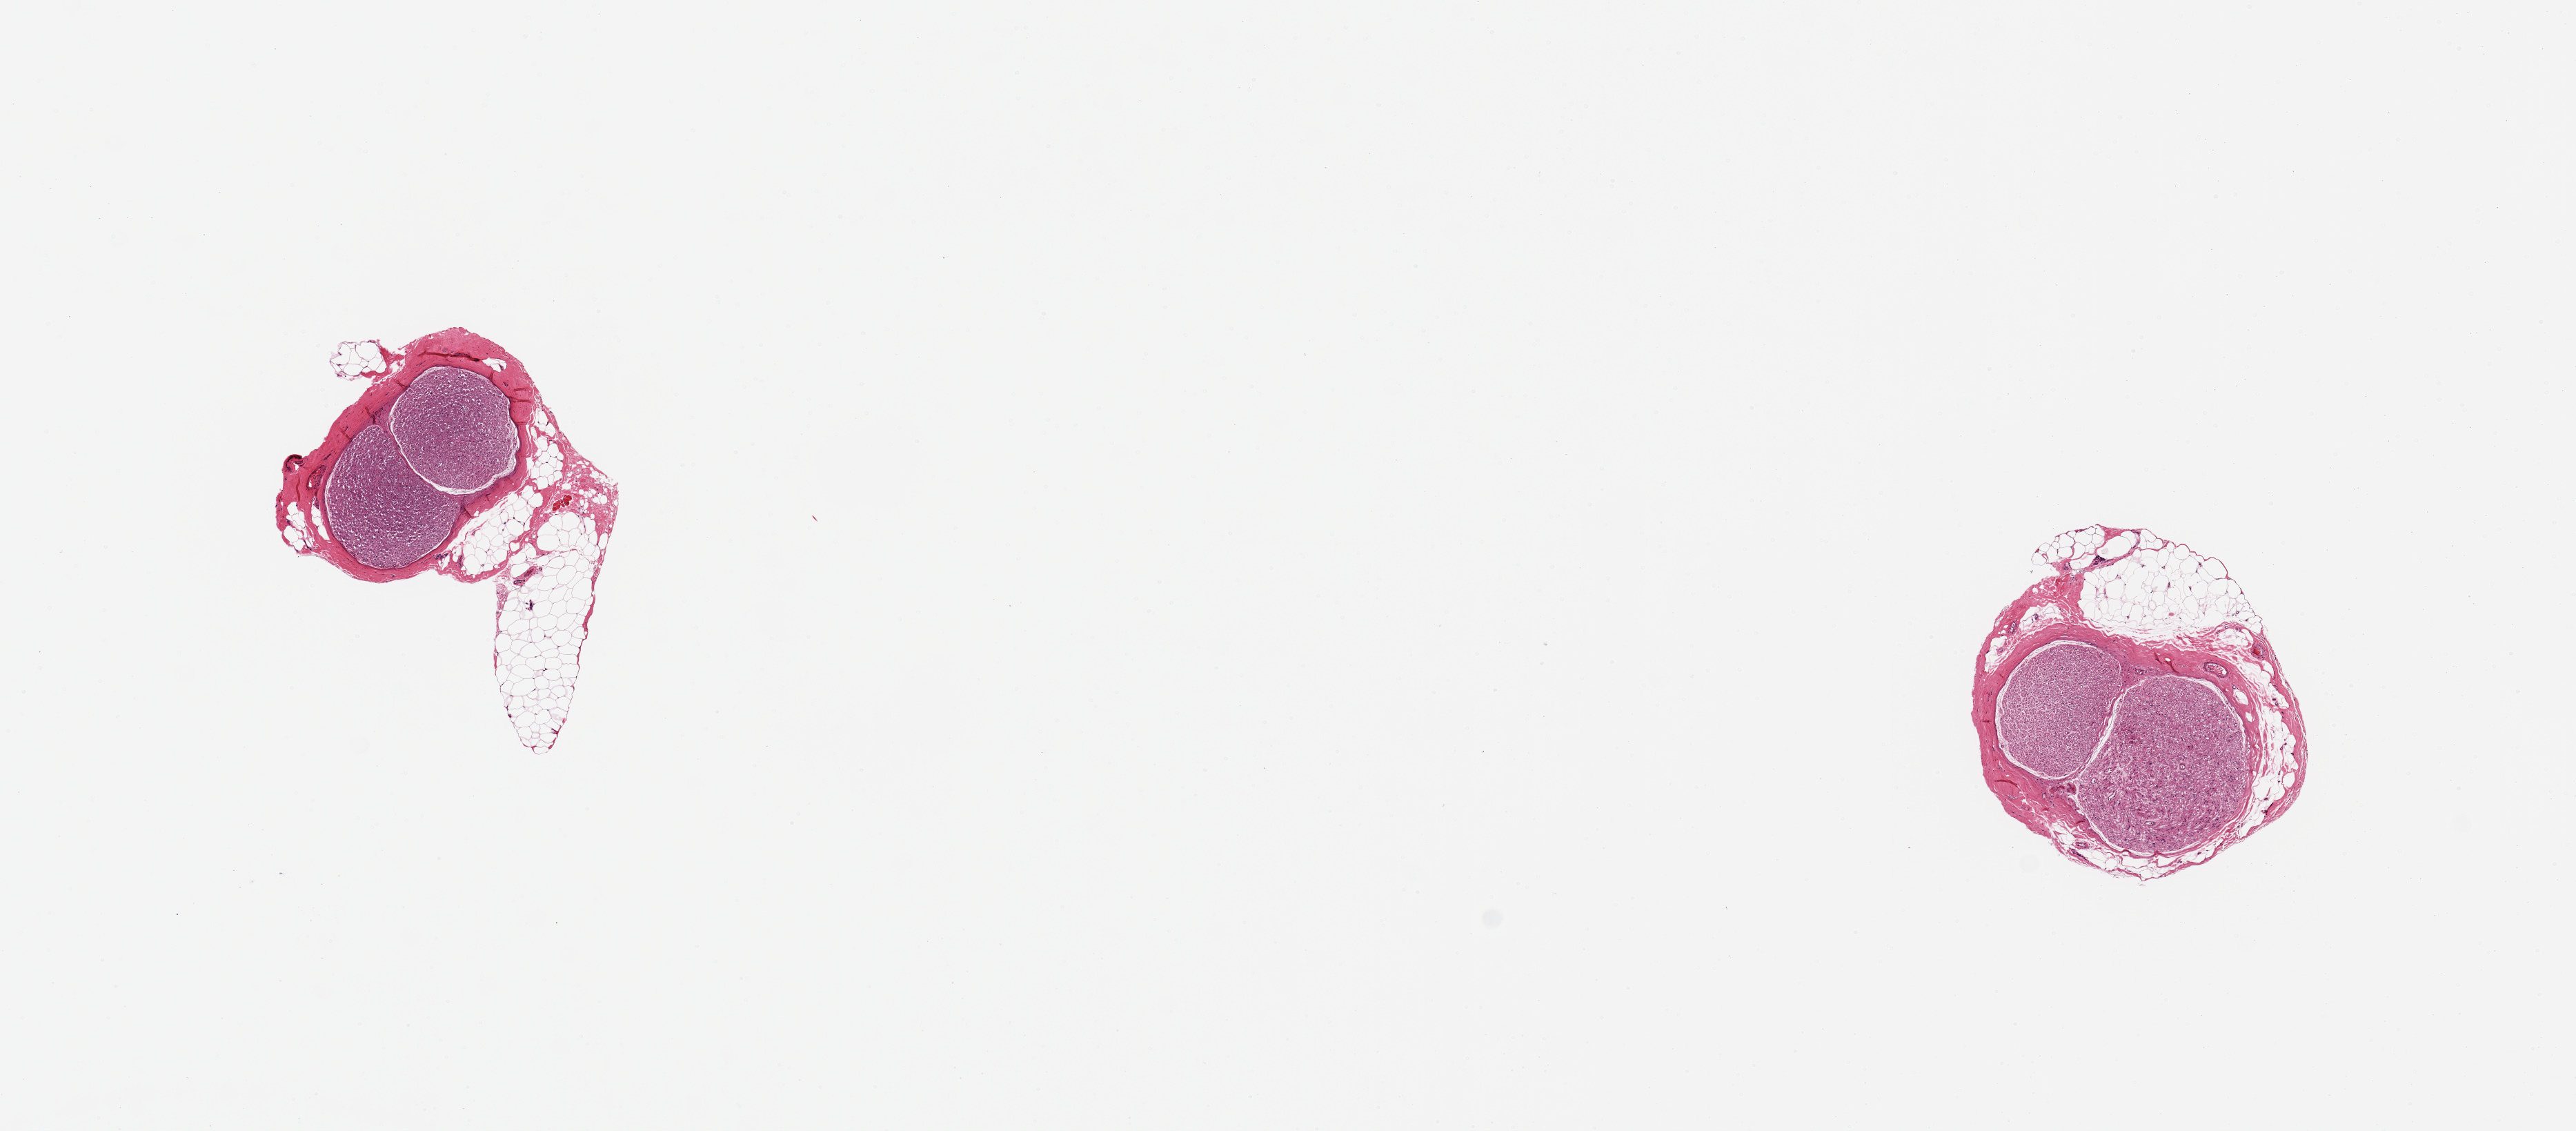
Whole-slide image, hematoxylin and eosin (H&E) stain, shown as a low-resolution overview of the whole scanned area (about 14.8 x 6.5 mm). PAXgene-fixed, paraffin-embedded tissue. Target tissue: tibial nerve. Donor tissue sample.
Reviewer comment on this tissue sample: 2 pieces, unusually poorly preserved. 1x2mm nerve is surround by fat/connective tissue, nerve is~40% of total specimen.